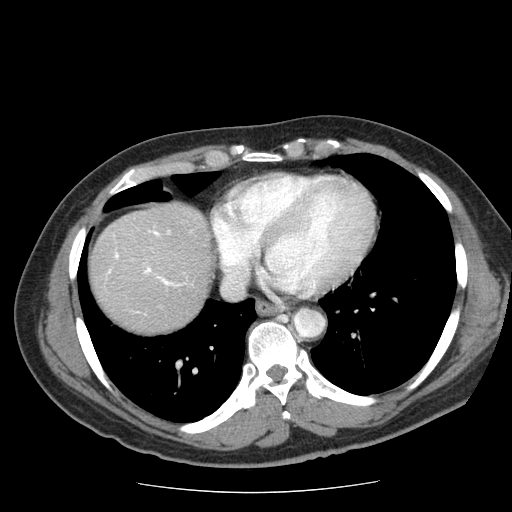
Contrast-enhanced abdominal CT (liver protocol), one axial slice; slice 68 of 85 in the series (ordered by position); reconstruction kernel STANDARD; soft-tissue window (W 400 / L 40 HU); 2.5 mm slice thickness; 512 × 512 image matrix, field of view 360 × 360 mm. Case-level facts recorded for this patient, not image findings: diagnosis: hepatocellular carcinoma (patient treated with transarterial chemoembolisation; whether this scan precedes or follows treatment is not stated here); TNM stage (as recorded): Stage-IIIA; Child-Pugh class: A; tumour differentiation: well differentiated.
Annotated regions visible in this slice (semi-automatic segmentation, software-assisted and operator-edited):
- liver parenchyma outside the tumour (the mass and vessels are separate outlines, so this box may not span the whole liver): box from (x=90, y=202) to (x=214, y=332) px
- liver vessels: (x=108, y=231)–(x=182, y=286)